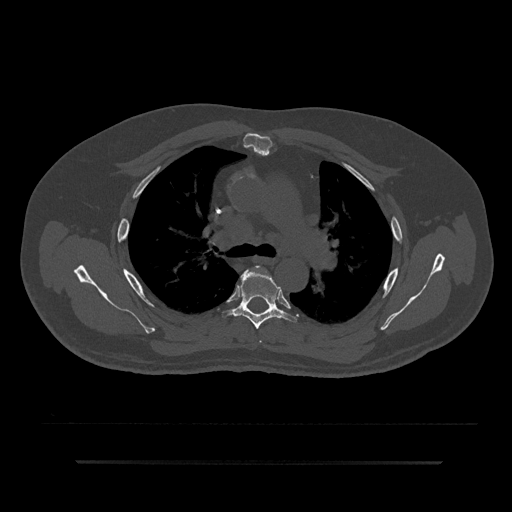
CT including the spine, one axial slice; position 578 of 797 along the scan axis; reconstruction kernel Br40s/3; 120 kVp; bone window (W 1800 / L 400 HU); 0.5 mm slice thickness; 512 × 512 image matrix. Male patient, age 59 years. Case-level facts recorded for this patient, not image findings: primary cancer: bile ducts.
Structures marked on this image (semi-automatically segmented with operator editing):
- T4 vertebra: bounding box <255,266,264,343> (left, top, right, bottom; pixels)
- T5 vertebra: <226,269,293,329>